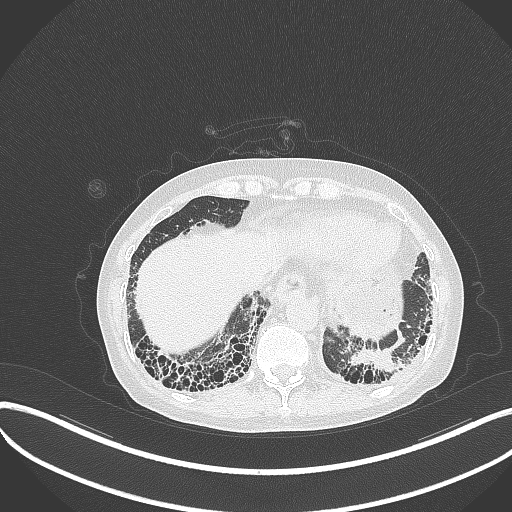
Chest CT, one axial slice; slice 60 of 373 in the series (ordered by position); reconstruction kernel B70f; 120 kVp; lung window (W 1500 / L -600 HU); 1 mm slice thickness; 512 × 512 image matrix. Patient: female, 56 years. From the clinical record (not read from this slice): clinical TNM (as recorded): T1 N0 M0.
Outlined on this slice (bounding box drawn by a radiologist):
- lung tumour (recorded histology: adenocarcinoma): bounding box [x1, y1, x2, y2] px = [352, 346, 397, 375]